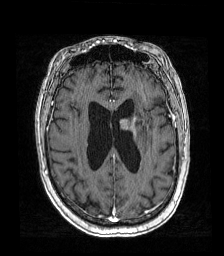
Brain MRI from a brain-tumour surgery series, one axial slice; position 66 of 192 along the scan axis; T1-weighted post-contrast; 1 mm slice thickness; 224 × 256 image matrix, field of view 219 × 250 mm. From the clinical record (not read from this slice): histopathology: Metastatic carcinoma from lung primary; tumour location: Left Frontal Caudate.
Annotated regions visible in this slice (manually delineated by an expert):
- tumour: bounding box (x1, y1, x2, y2) in pixels: (117, 116, 148, 136)